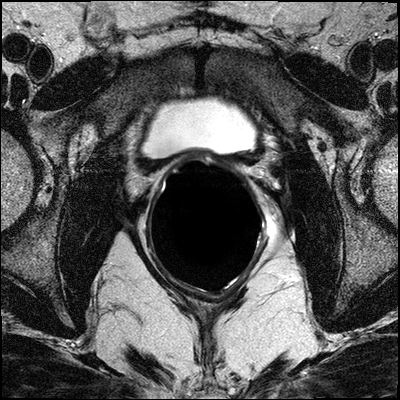
Pelvic MRI after prostatectomy (prostatic bed); 3 images, each a single mid-volume slice chosen by position (not for content). Treatment context recorded for this patient: post op.
Image 1: T2-weighted axial slice, series "T2W_TSE_AX", slice 20 of 38, 3 mm slice thickness.
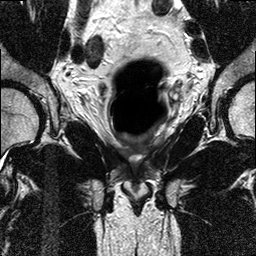
Image 2: coronal T2-weighted image, slice 17 of 32, 3 mm slice thickness.
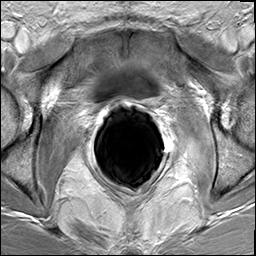
Image 3: axial dynamic contrast-enhanced (DCE) T1-weighted image, series "dyn_THRIVE", slice 21 of 40, dynamic phase 5 of 8, 6 mm slice thickness.
MRI report (verbatim):
Regular surgical bed. Regular appearance of the anastomosis. No definite masses seen within the prostatic bed. No foci of suspicious enhancement in and around the prostatic bed. Unremarkable urinary bladder. There are remnant seminal vesicles present - on both sides. No suspiciously enlarged obturator and iliac lymph nodes. The visualized osseous structures without evidence of metastasis IMPRESSION: No suspicious mass. No enlarged obturator or iliac lymph nodes. Normal appearance of the prostatic bed and anastomosis. There are remnant seminal vesicles bilateral.

Biopsy pathology report for this patient (as recorded):
Consult with past prostatectomy. At operation 4 yrs ago, Gleason 4+4=8 prostatic adenocarcinoma with bilateral seminal vesicle invasion and extensive perineural invasion. Two right-sided pelvic LNs and two left-sided pelvic LNs were negative, although it seems they contained some sort of hyperplasia. He had a PSA of 0.3 in last yr, and reportedly had one shot of lupron. His PSA in 2 mos later remained 0.3. CT of the A/P on 2 mos ago revealed no evidence of metastases, but noted residual seminal vesicle tissue and scattered subcentimeter pelvic lymph nodes. Repeat PSA on 1 mo ago was 1.9. No further op recomended